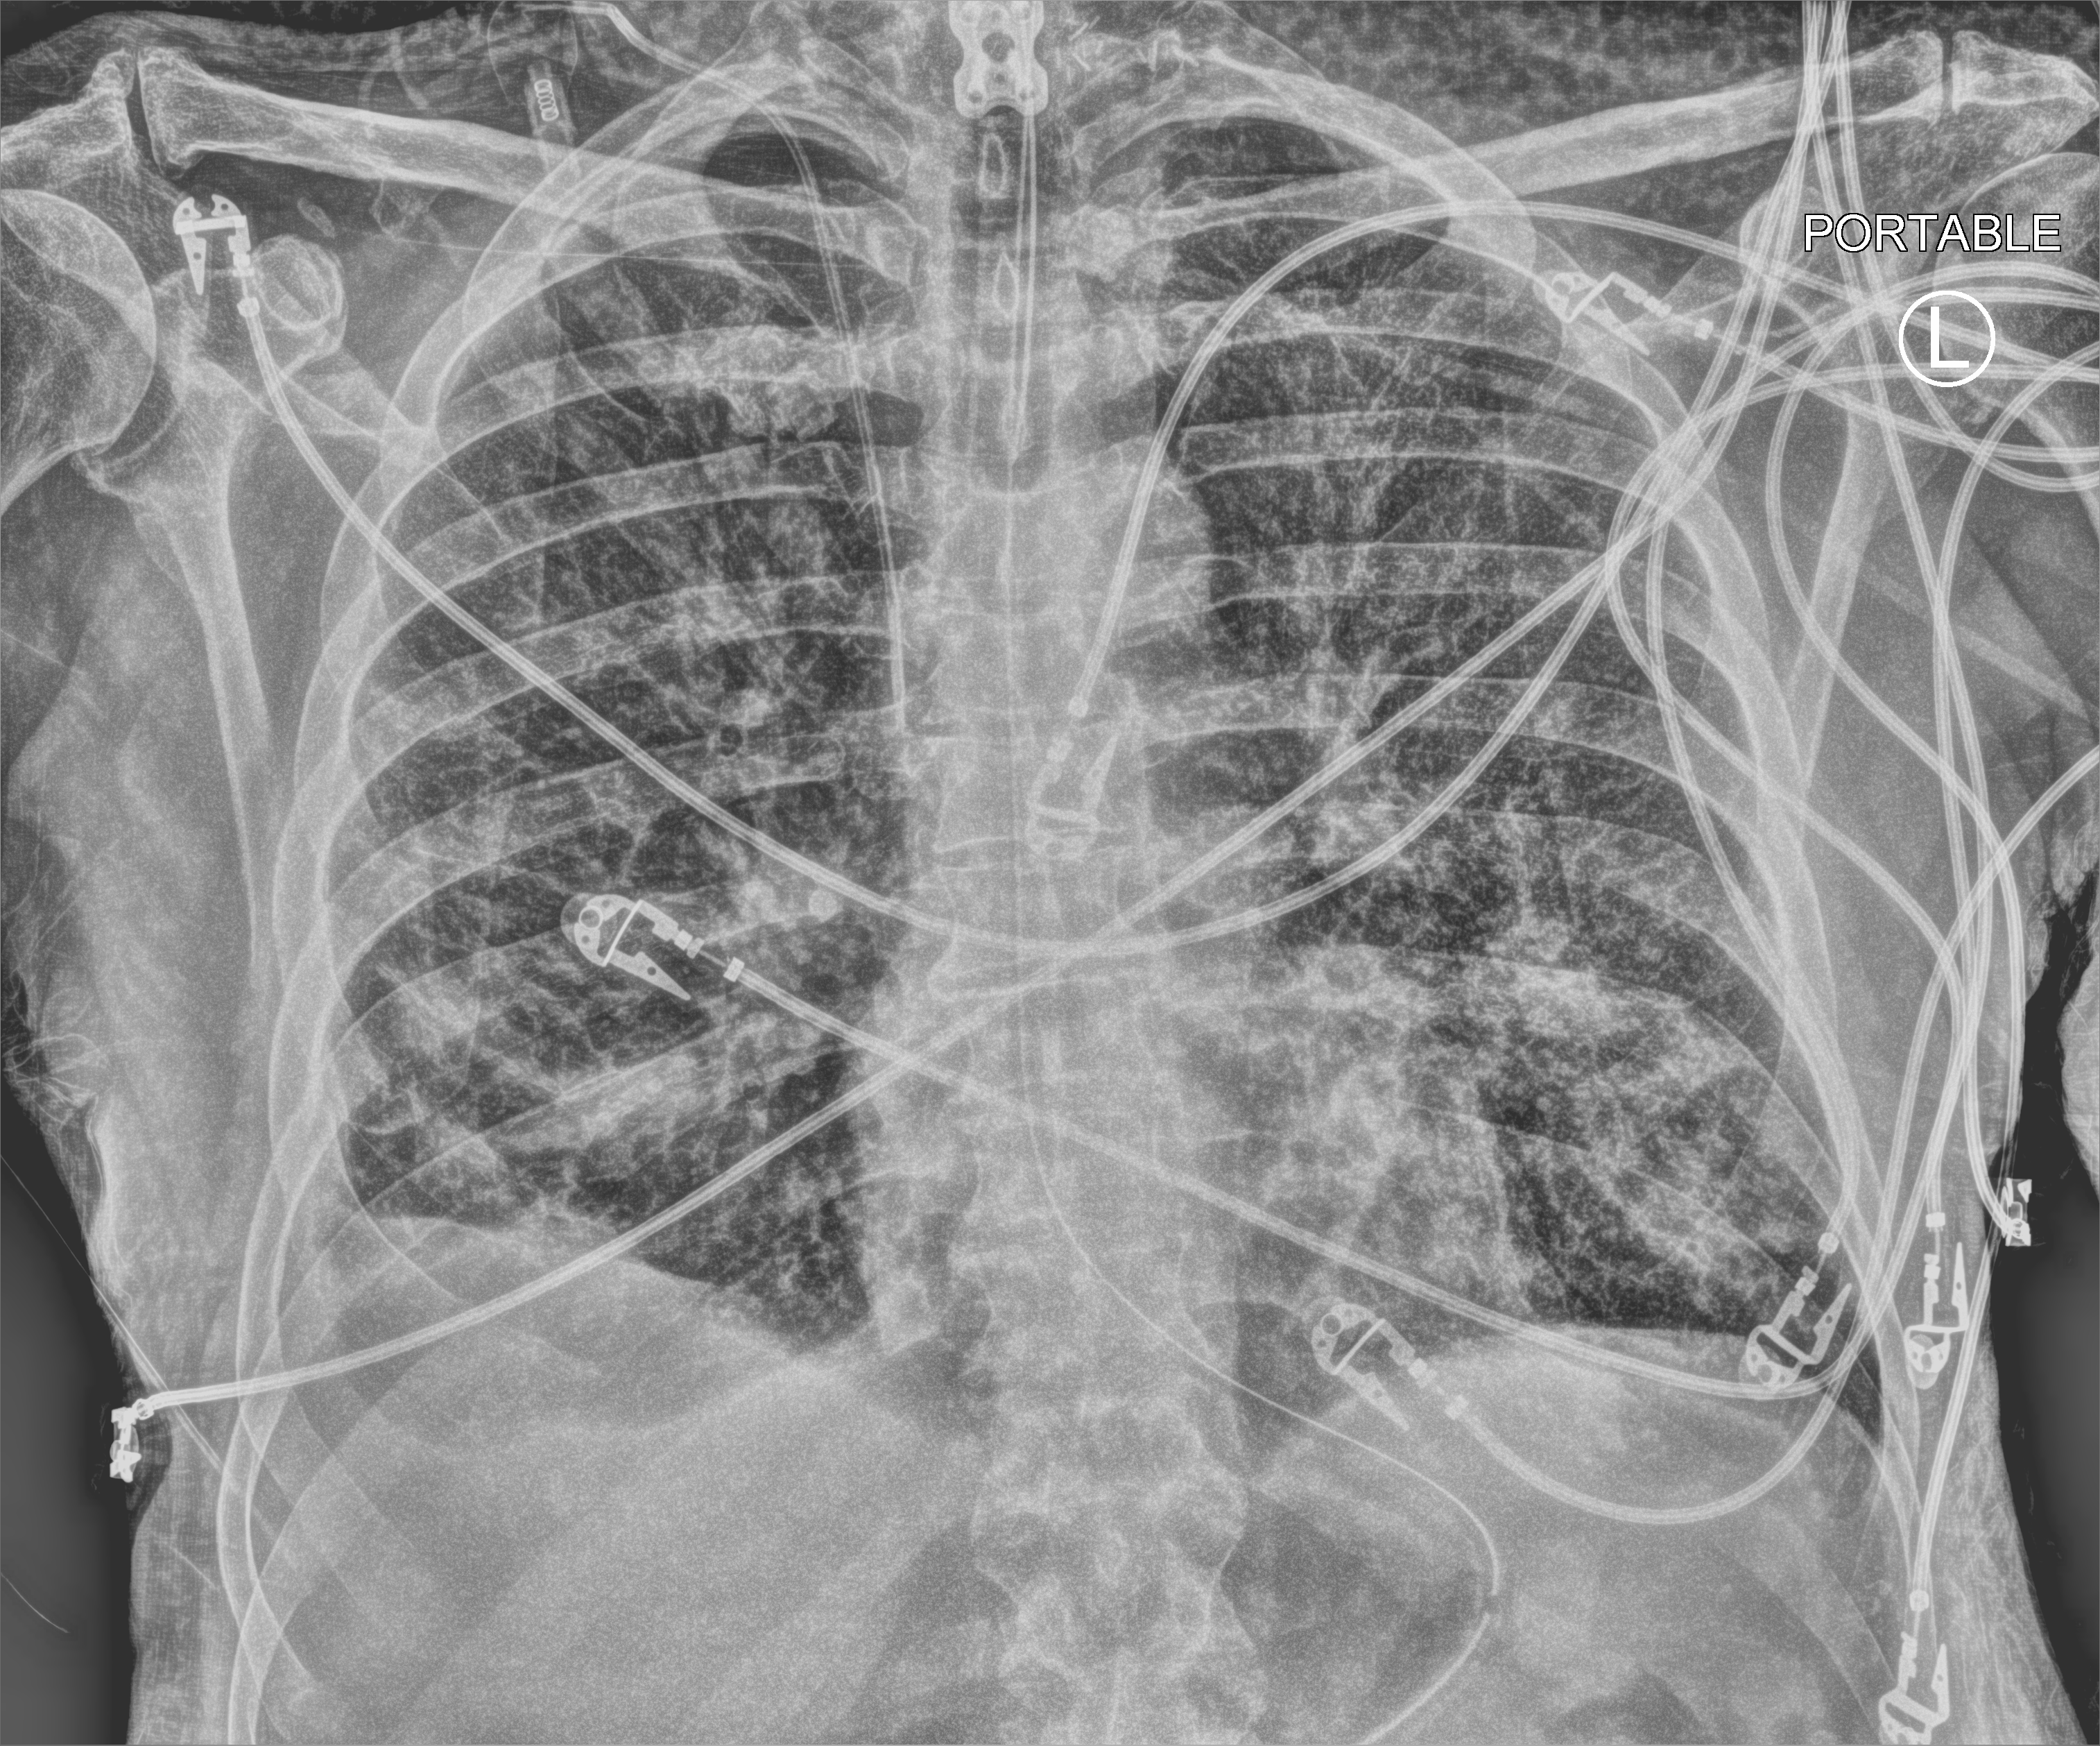
Bedside chest radiograph (computed radiography); anteroposterior (AP) projection. Male patient hospitalised with COVID-19, age 60–74 years.
Hospital-stay facts (about this admission, not read from this image; timing relative to this image not recorded): mechanically ventilated during this hospital stay: yes; admitted to intensive care during this hospital stay: yes.